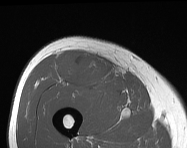
MRI of an extremity soft-tissue mass, one axial slice; slice 68 of 114 in the series (ordered by position); MR volume resampled by the dataset authors to the PET/CT grid (not the native acquisition matrix); 3.27 mm slice thickness; 187 × 148 image matrix. Male patient. Case-level facts recorded for this patient, not image findings: histological type: pleiomorphic leiomyosarcoma; grade: intermediate; site of the primary tumour: right thigh.
Structures marked on this image (expert contour drawn on MRI and transferred to this co-registered scan by the dataset authors):
- gross tumour volume including surrounding oedema: bounding box [x1, y1, x2, y2] px = [57, 52, 112, 87]
- gross tumour volume (mass): [70, 59, 106, 85]